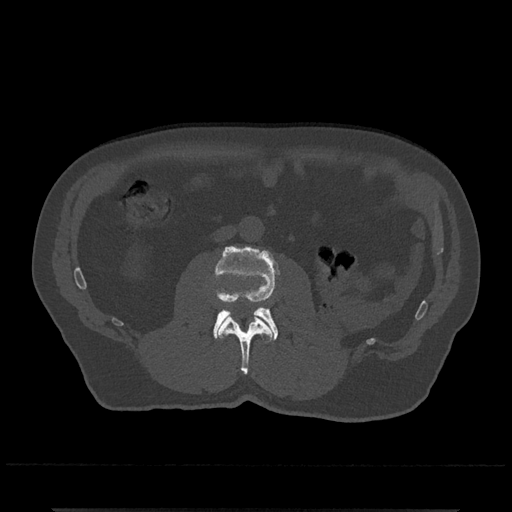
CT including the spine, one axial slice. Slice 258 of 797 in the series (ordered by position). Bone window (W 1800 / L 400 HU). 512 × 512 image matrix. Male patient, age 67 years. Case-level facts recorded for this patient, not image findings: primary cancer: prostate.
Annotated regions visible in this slice (semi-automatic segmentation, software-assisted and operator-edited):
- L2 vertebra: box from (x=219, y=315) to (x=273, y=375) px
- L3 vertebra: (x=213, y=246)–(x=279, y=341)